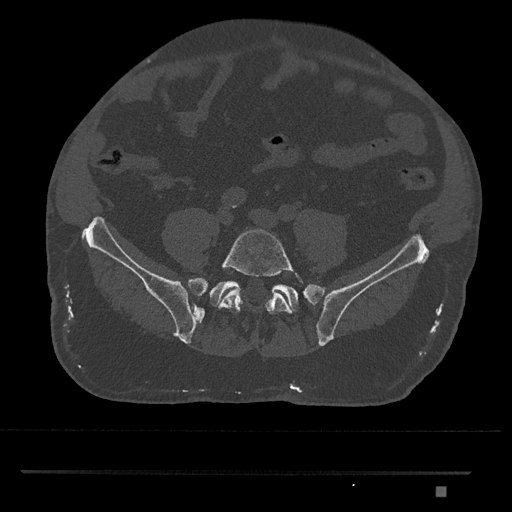
CT including the spine, one axial slice; position 541 of 1134 along the scan axis; bone window (W 1800 / L 400 HU); 0.5 mm slice thickness; 512 × 512 image matrix. Patient: male, 65 years. Case-level facts recorded for this patient, not image findings: primary cancer: prostate.
Structures marked on this image (semi-automatic segmentation, software-assisted and operator-edited):
- L5 vertebra: bounding box <219,227,304,325> (left, top, right, bottom; pixels)